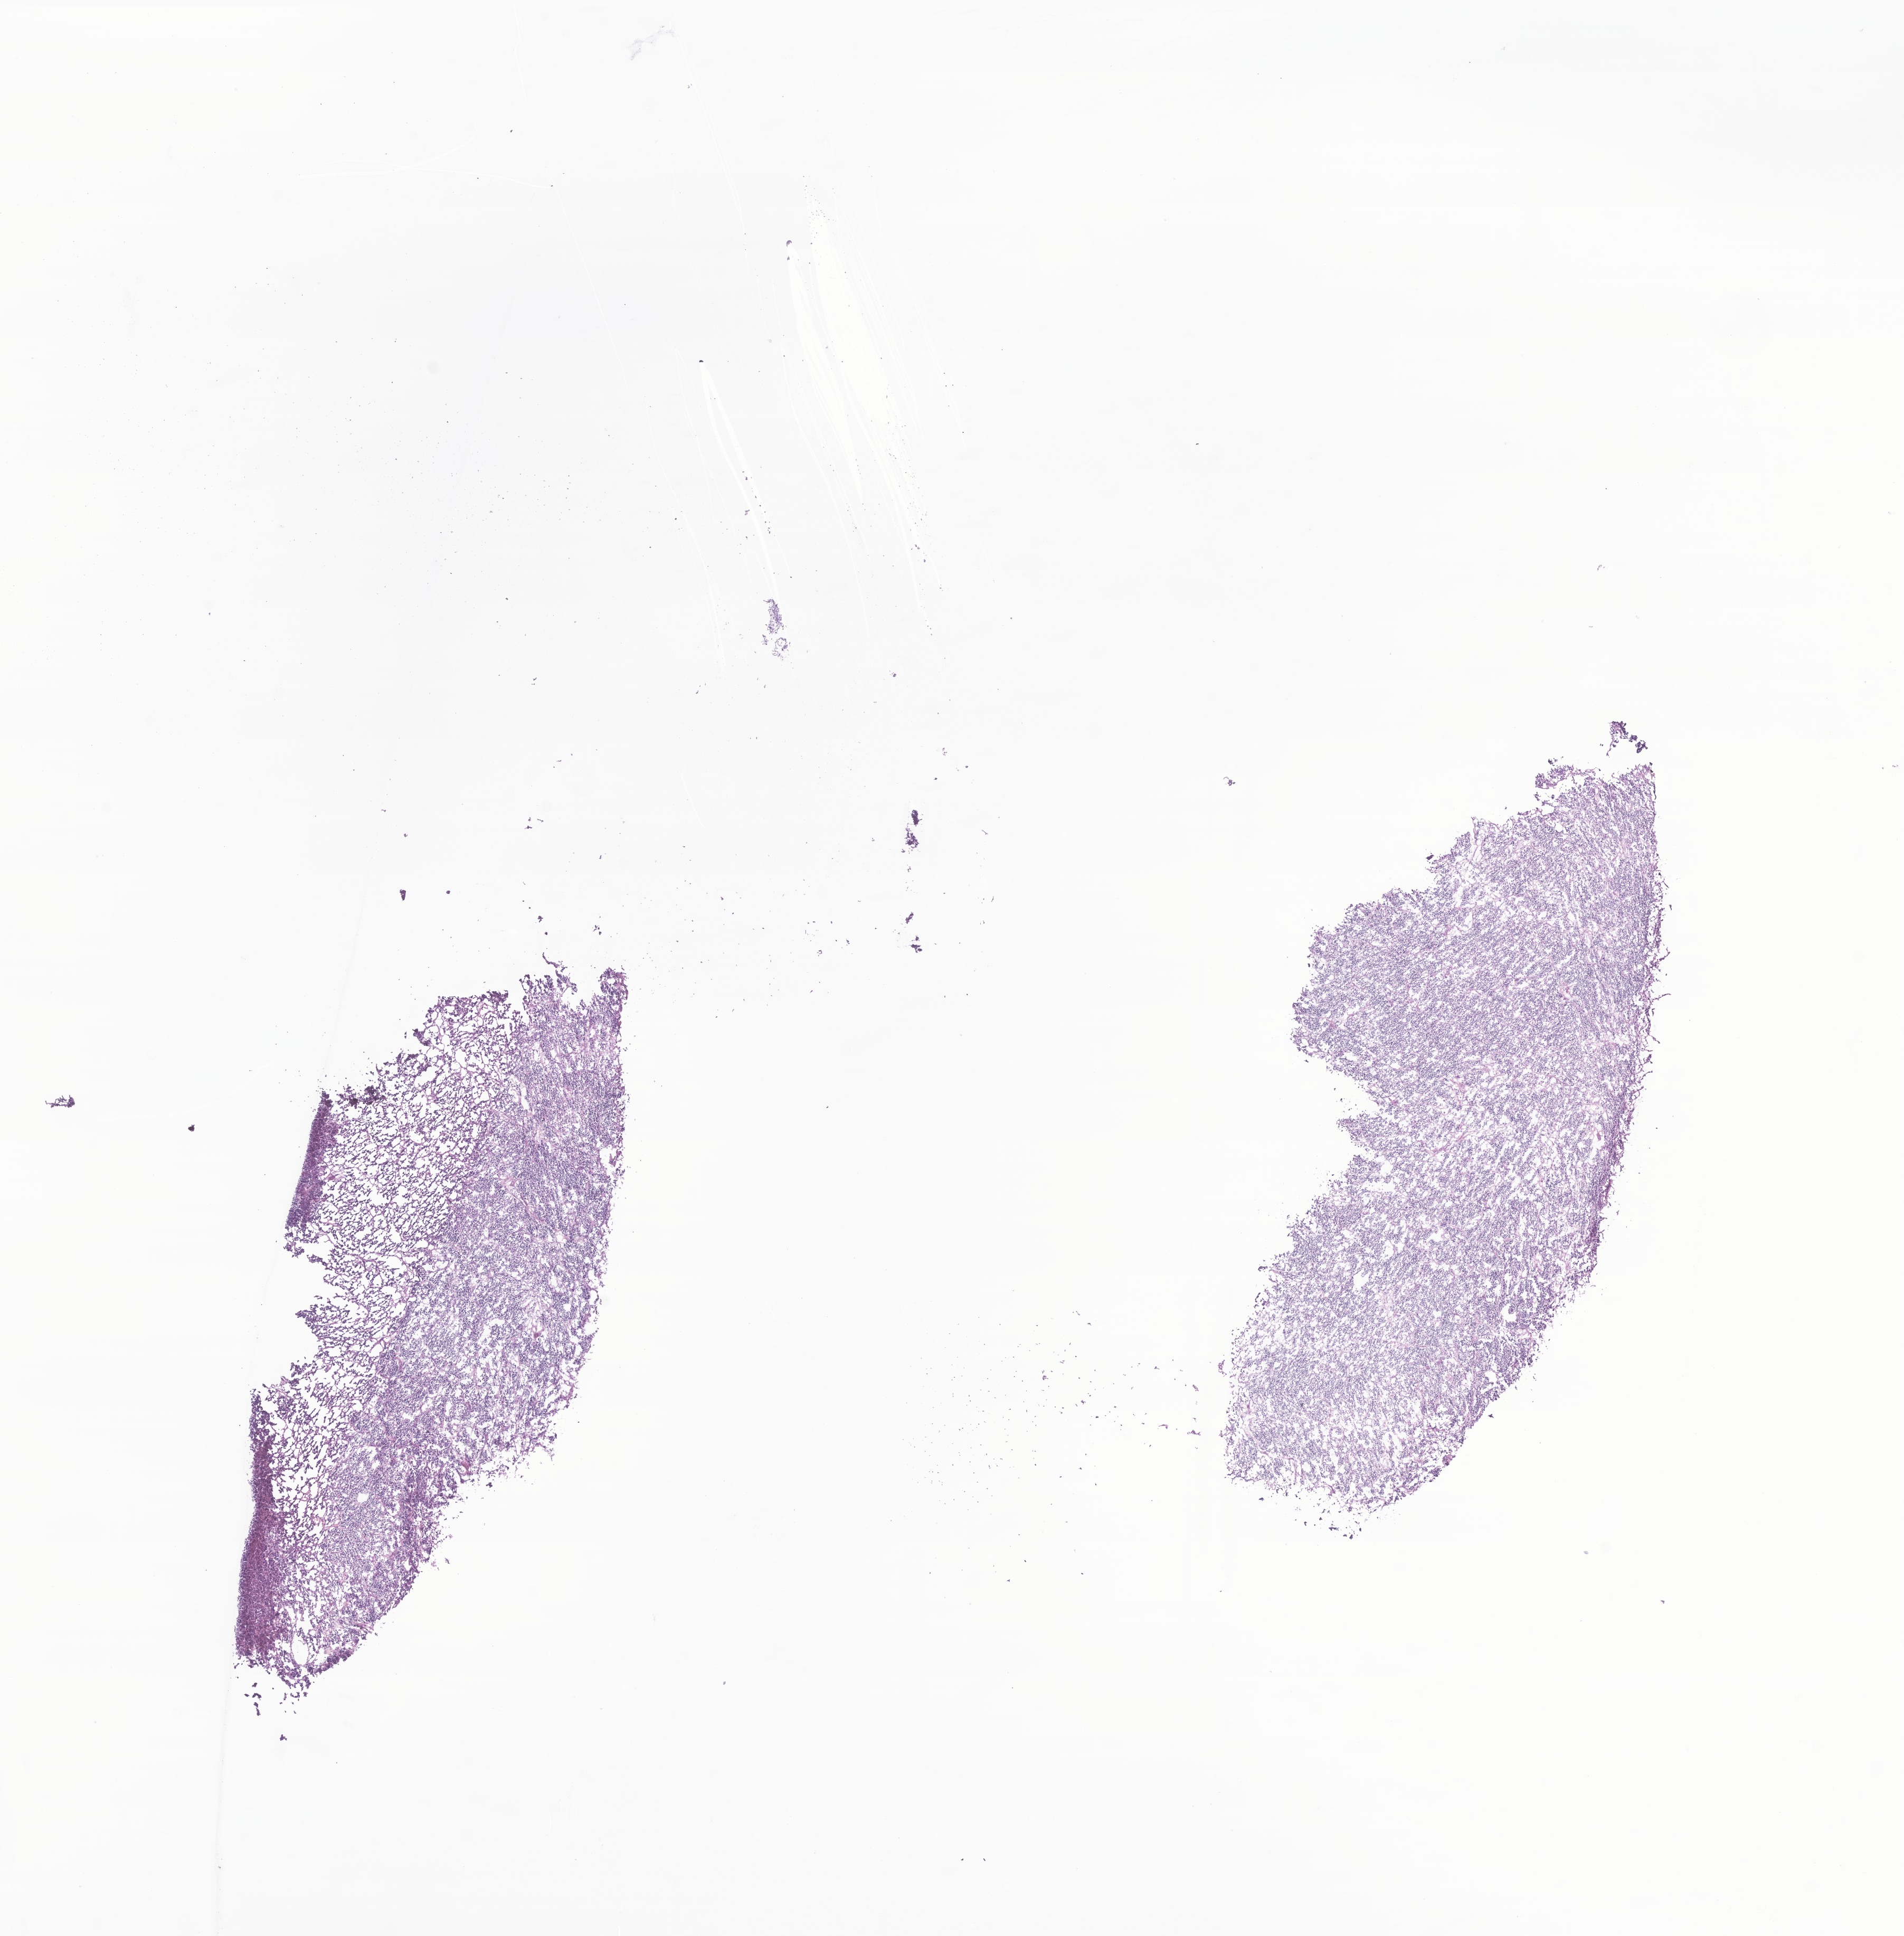
Digitized hematoxylin and eosin (H&E)-stained section of tumor tissue from the adrenal gland, shown as a low-resolution overview of the whole scanned area (about 15.2 x 15.5 mm). Frozen section (OCT-embedded). Patient male; age 129 days.
Diagnosis: Neuroblastoma, NOS.